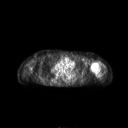
FDG PET of an extremity soft-tissue mass (from a PET/CT study), one axial slice; slice 178 of 267 in the series (ordered by position); 3.27 mm slice thickness; 128 × 128 image matrix. Patient: female, 83 years. From the clinical record (not read from this slice): histological type: pleiomorphic leiomyosarcoma; grade: high; site of the primary tumour: left biceps.
Outlined on this slice (expert contour drawn on MRI and transferred to this co-registered scan by the dataset authors):
- gross tumour volume including surrounding oedema: bounding box (x1, y1, x2, y2) in pixels: (91, 62, 101, 76)
- gross tumour volume (mass): (91, 62, 101, 73)